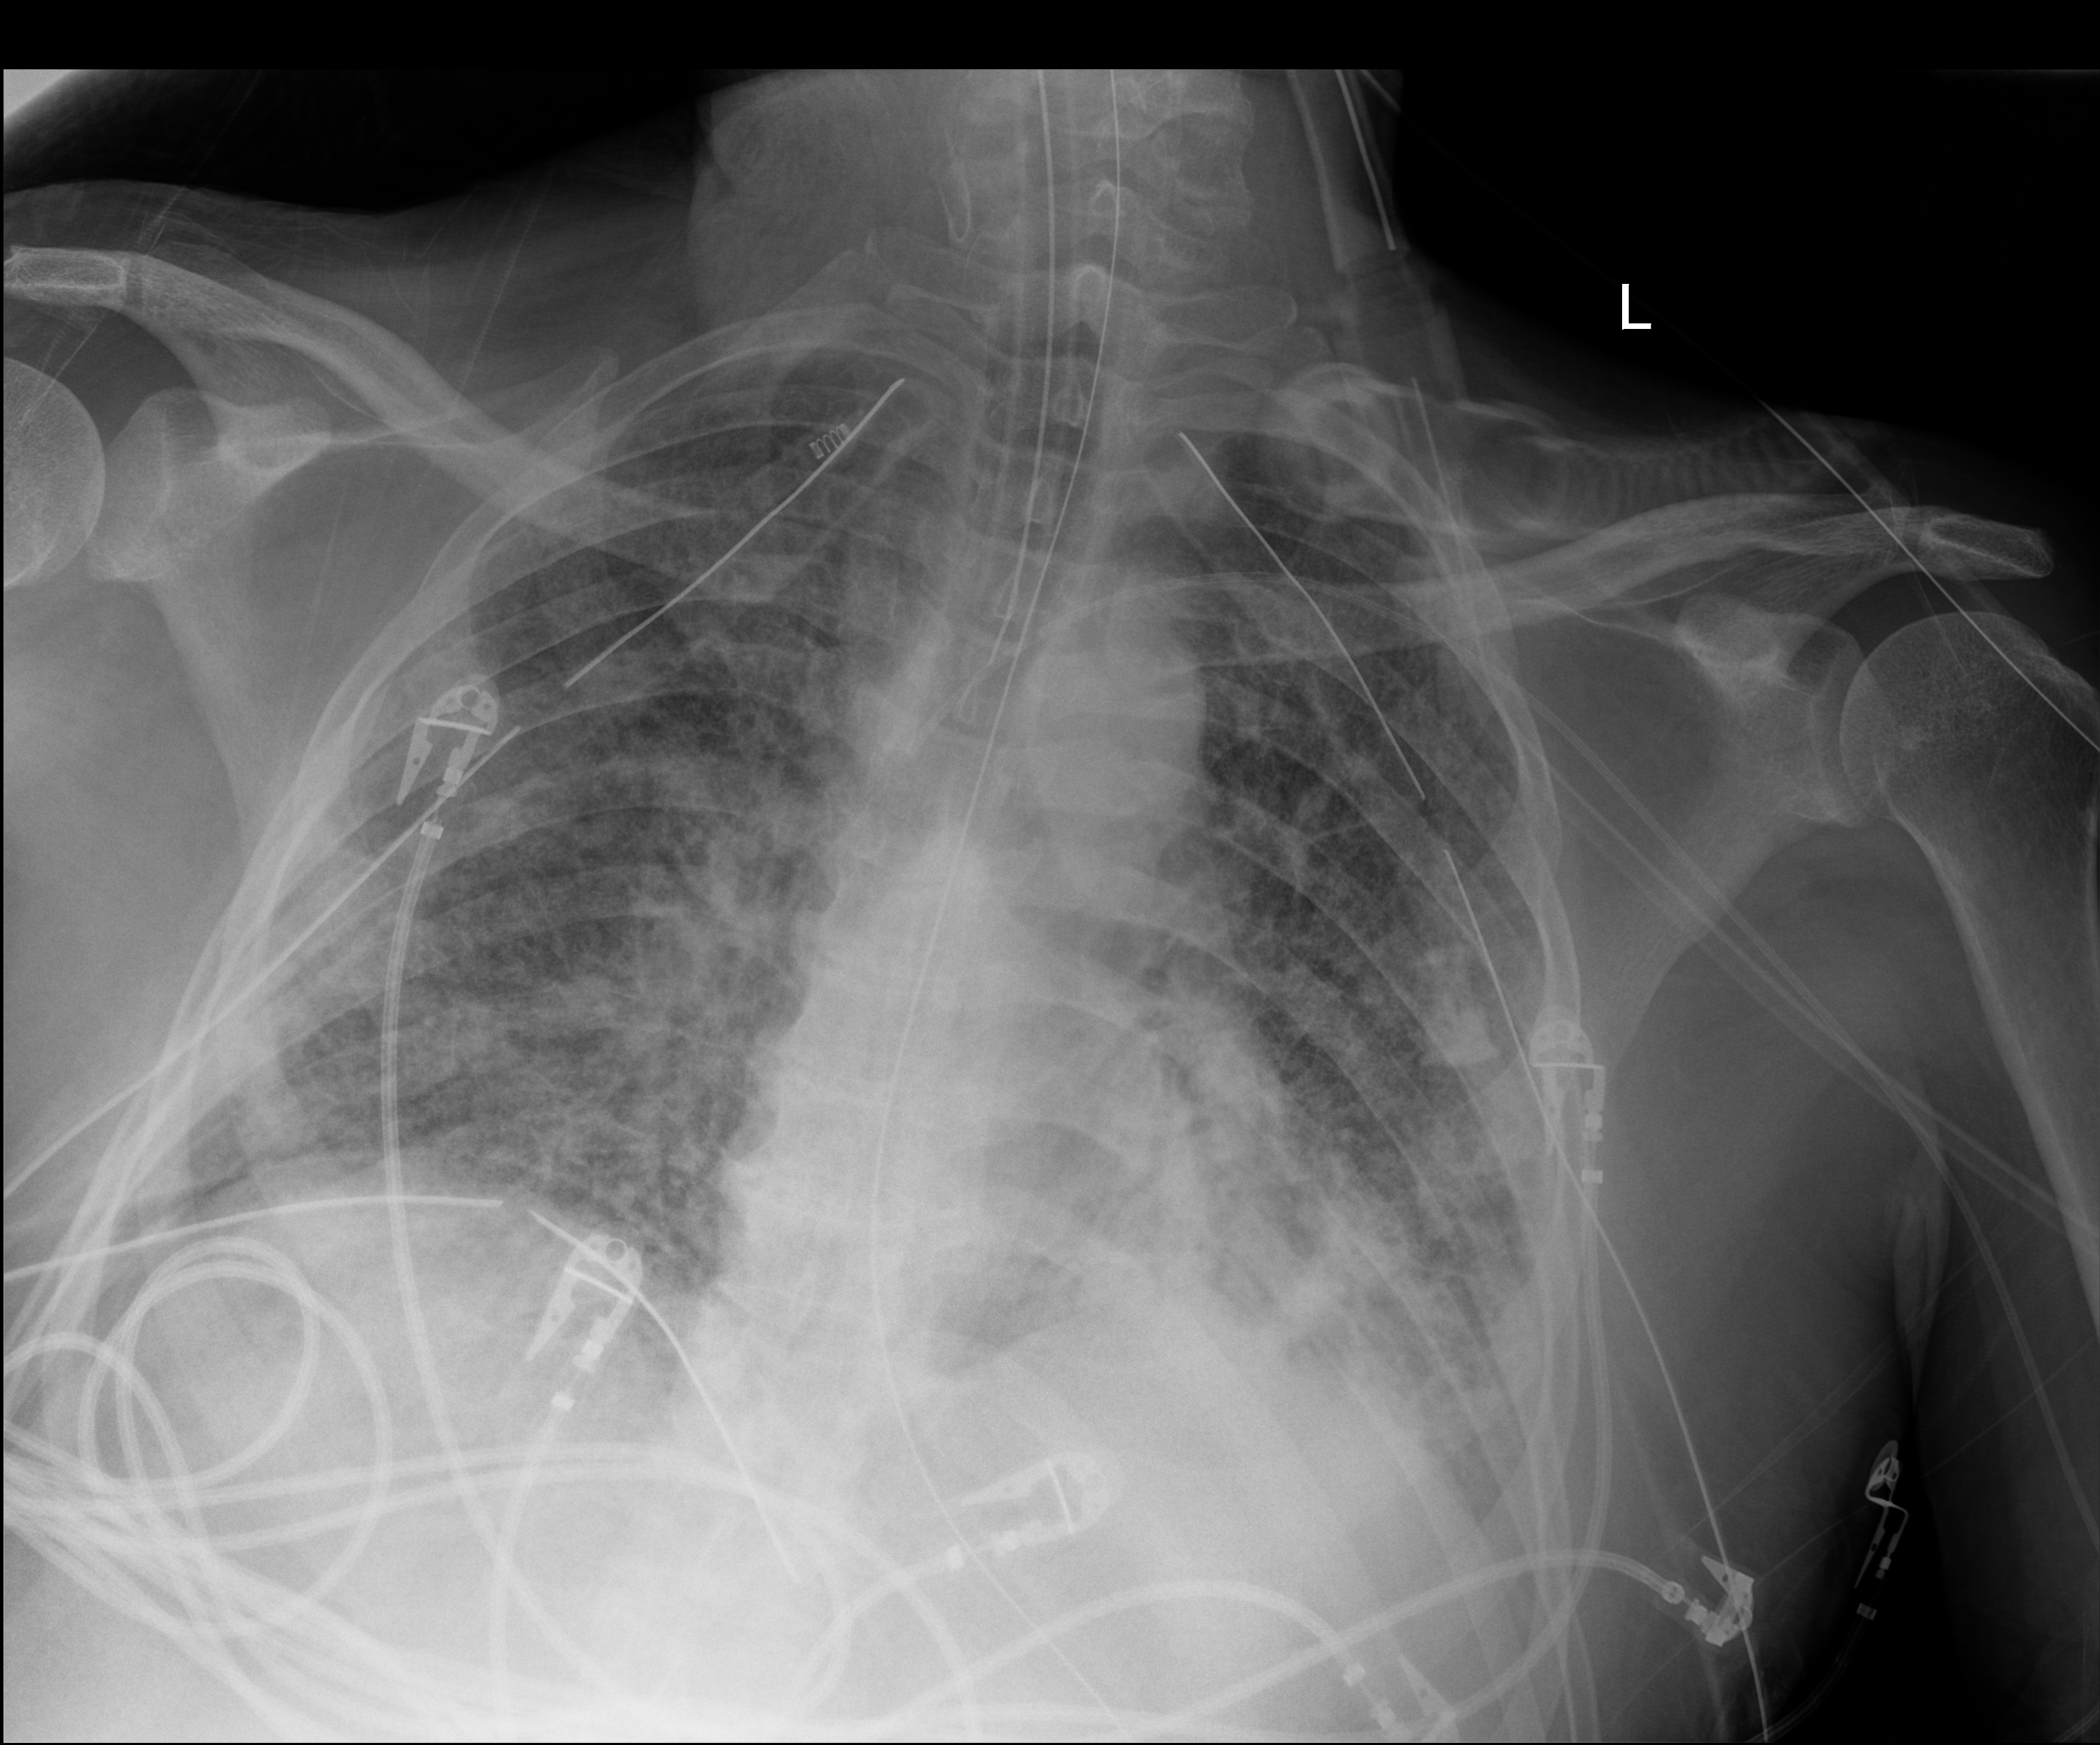
Portable chest radiograph; anteroposterior (AP) projection. Patient hospitalised with COVID-19; male, aged 18–59 years.
From the hospital-stay record, not from the radiograph (when in the stay this image was taken is not recorded):
- COPD (admission record): no